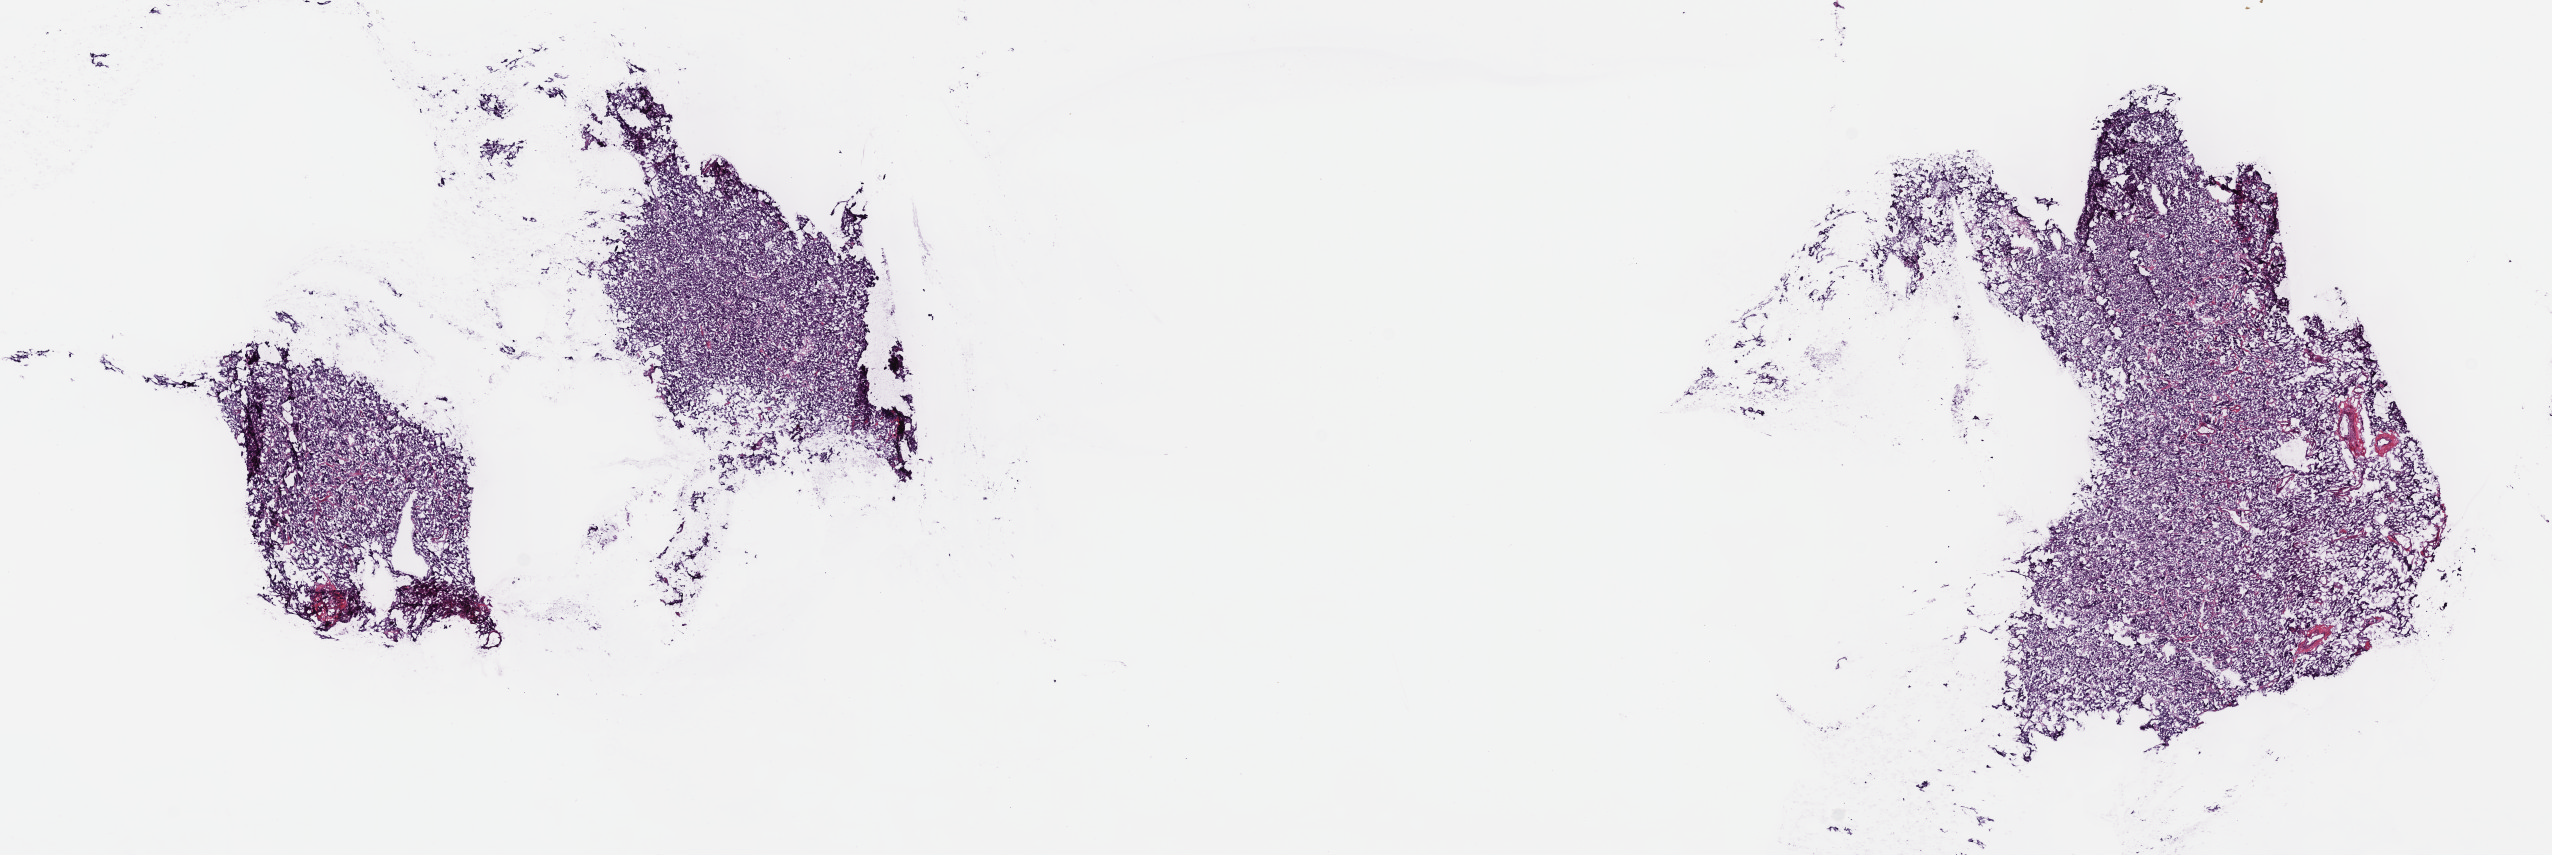
Whole-slide histology image, H&E-stained — shown as a low-resolution overview of the whole scanned area (about 20.6 x 6.9 mm), frozen section from the top of the tissue portion, sample: primary tumour, adrenal gland. Male, age 41 years at initial diagnosis. Slide review estimates, as recorded: tumour cells 90%, tumour nuclei 90%.
Diagnosis: Pheochromocytoma, NOS.